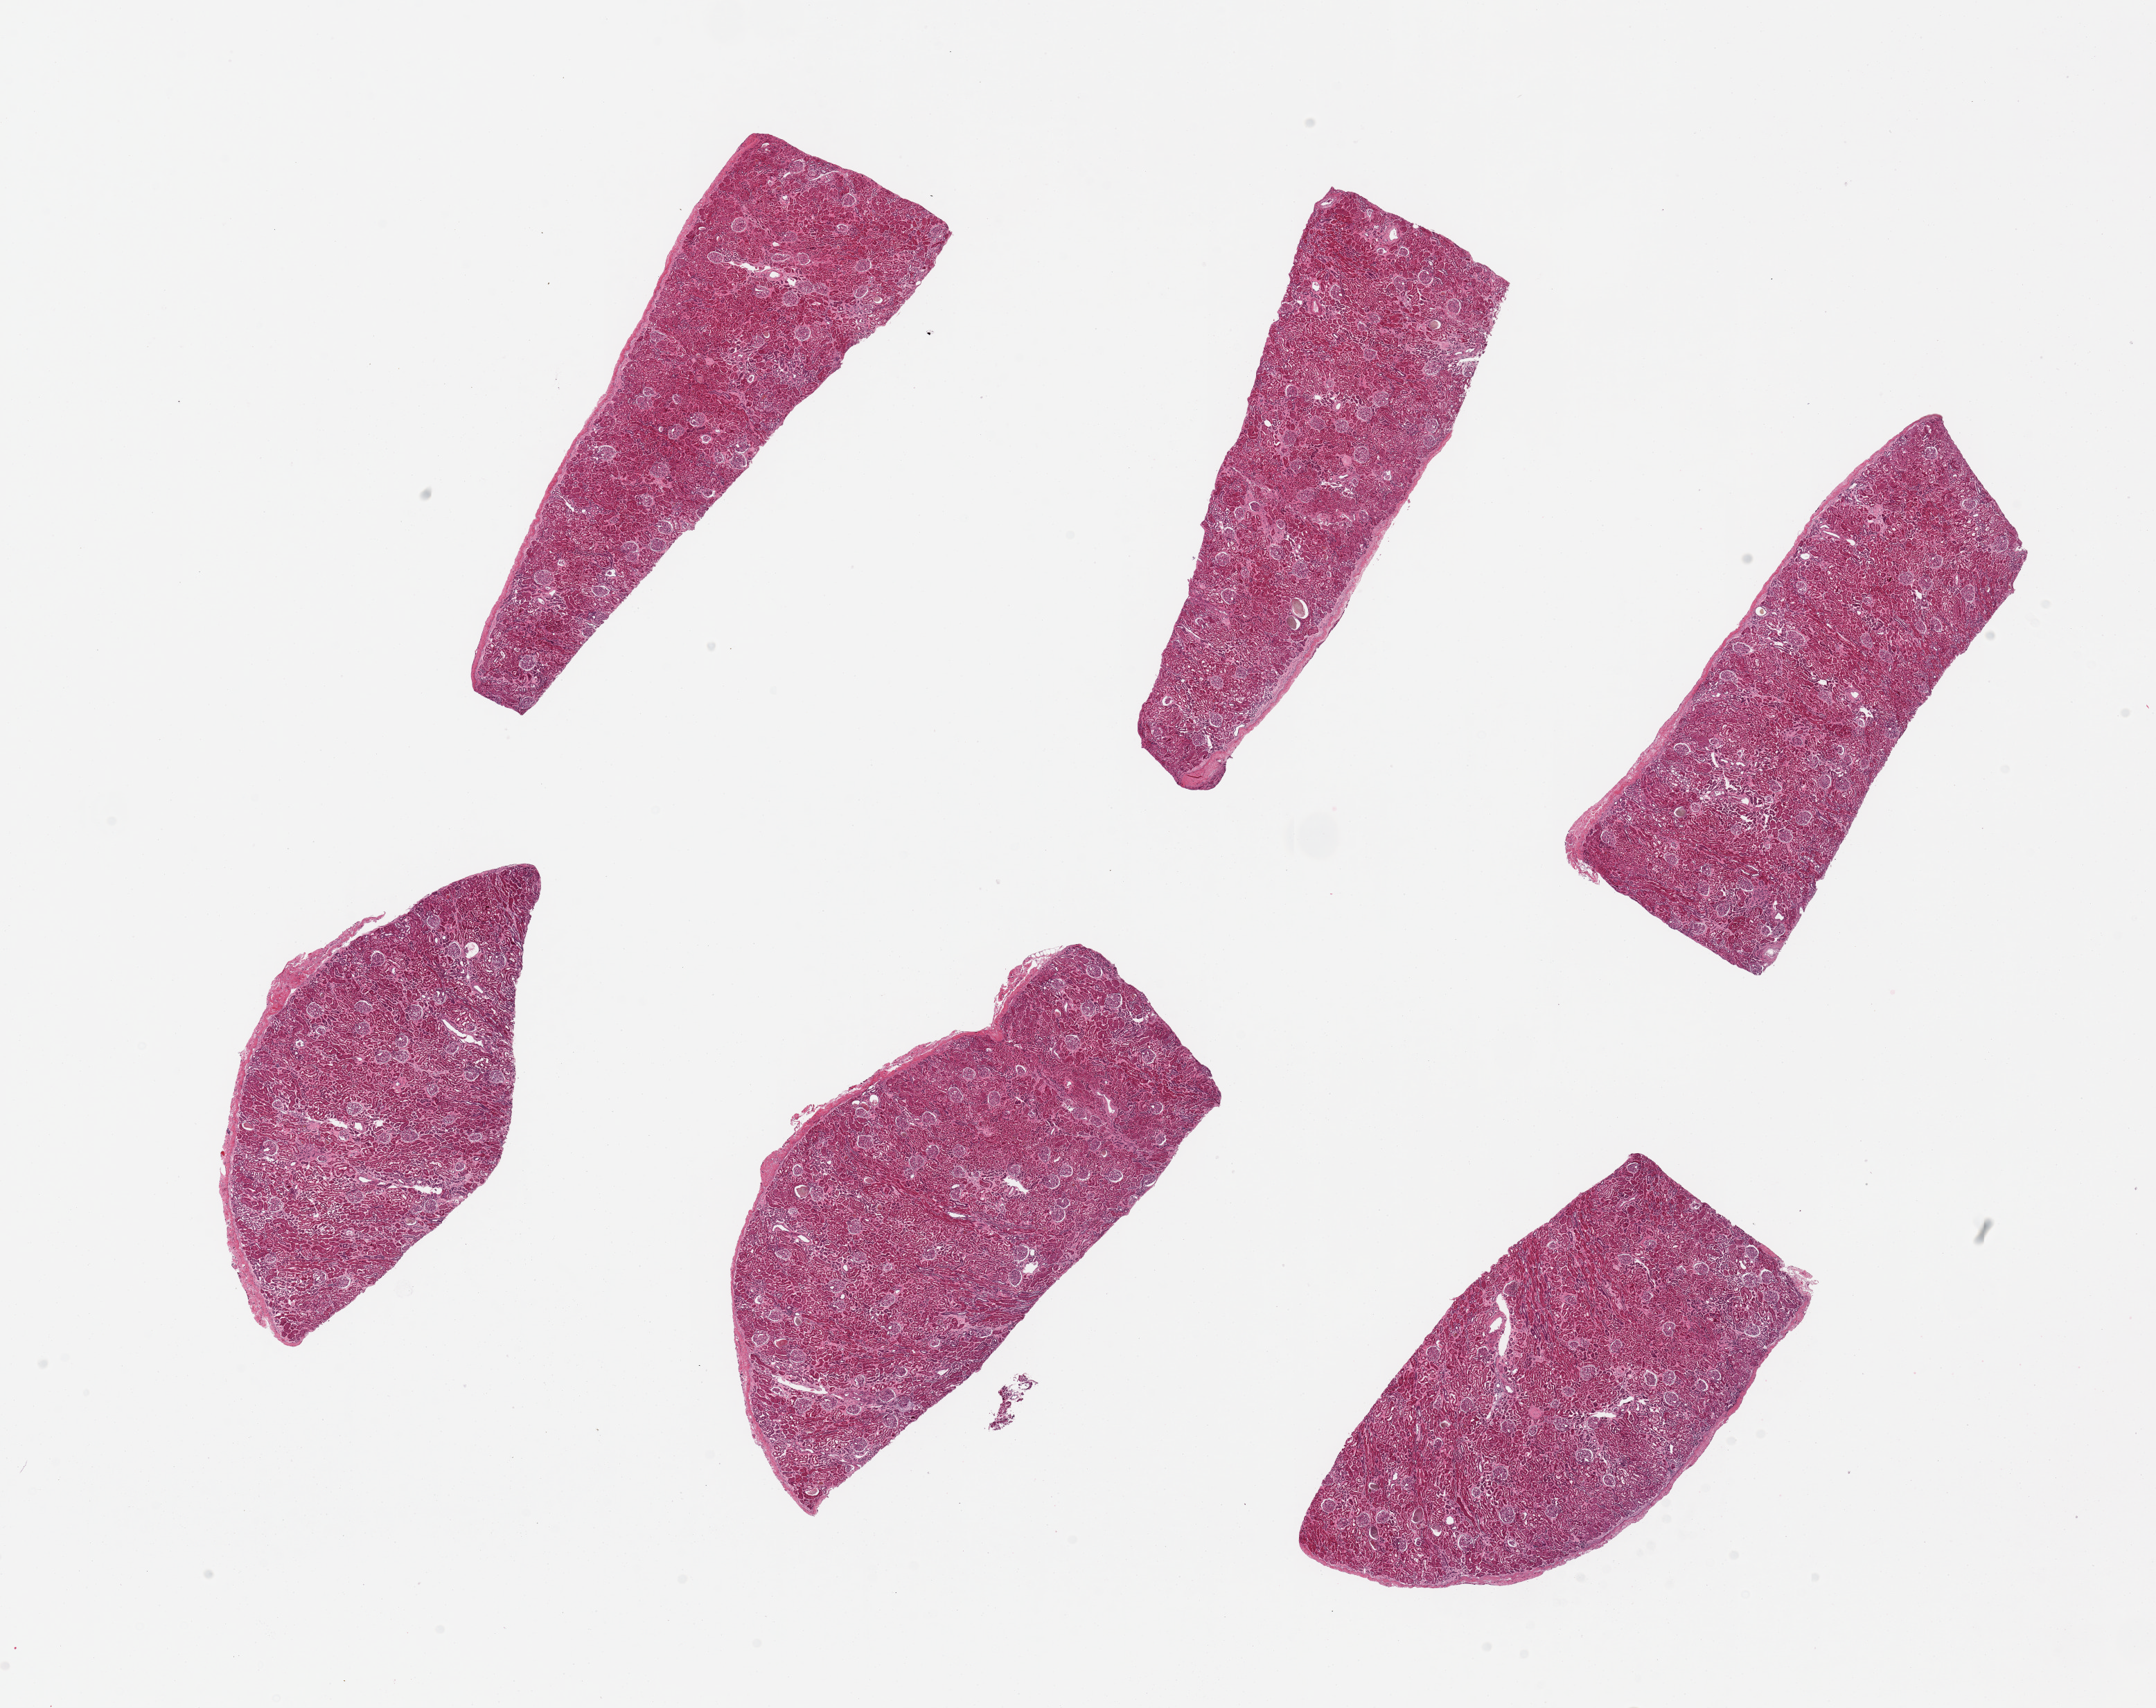
Hematoxylin and eosin (H&E) whole-slide image, brightfield, whole scanned area (about 24.6 x 19.5 mm, acquisition: 20x scan) shown as a low-resolution overview. PAXgene-fixed paraffin-embedded (PFPE) section. Target tissue: renal cortex. Donor tissue sample. Male donor.
Review note (as recorded): 6 pieces, up to 7x3mm; no vascular sclerosis; mild nonspecific increase in glomerular mesangial matrix, but no glomerular sclerosis.